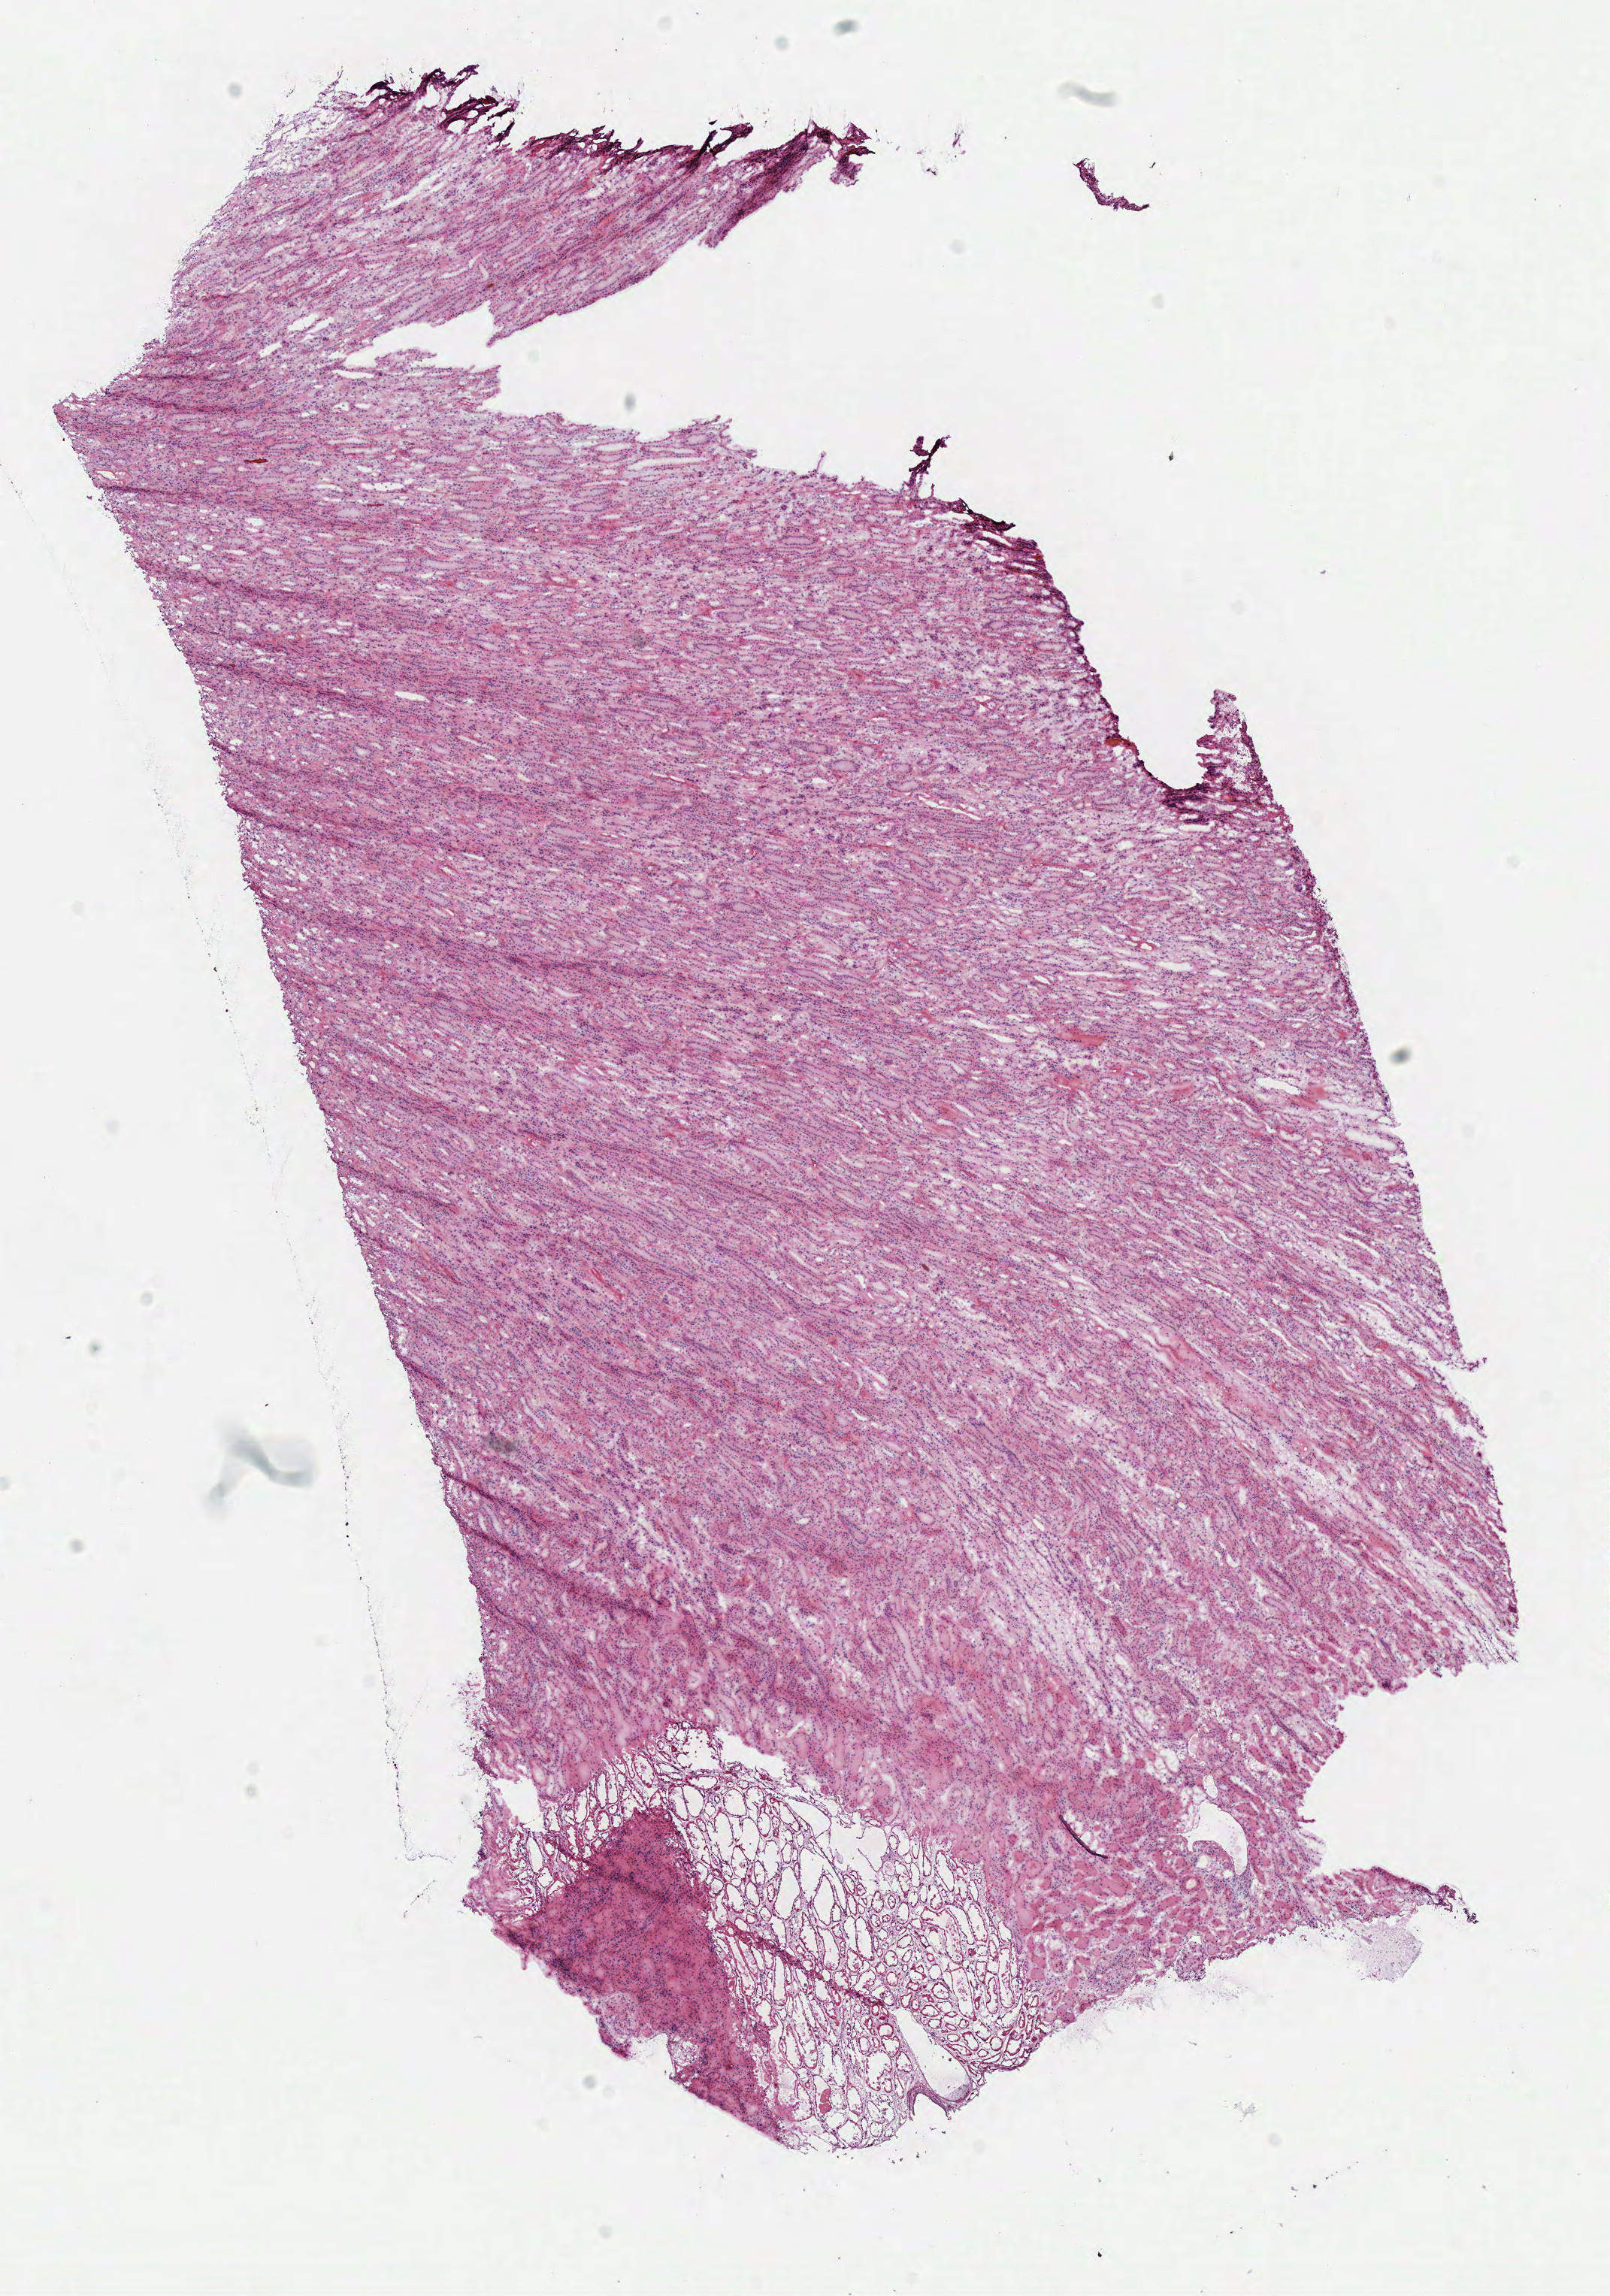
Whole-slide histology image, H&E — a low-resolution overview of the entire scanned area, about 8.4 x 12.0 mm. Frozen section from the top of the tissue portion. Solid tissue normal (non-tumour tissue) sample from the kidney. Patient: male, age at initial diagnosis 60 years.
This section: solid tissue normal sample (biorepository sample class). Patient diagnosis: Clear cell adenocarcinoma, NOS.